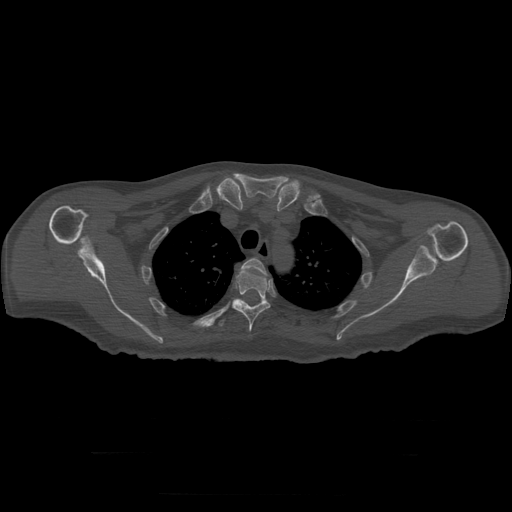
CT including the spine, one axial slice. Position 242 of 397 along the scan axis. Reconstruction kernel STANDARD. Bone window (W 1800 / L 400 HU). 1.25 mm slice thickness. 512 × 512 image matrix, field of view 510 × 510 mm. Patient age 73 years. From the clinical record (not read from this slice): primary cancer: prostate.
Outlined on this slice (semi-automatically segmented with operator editing):
- T3 vertebra: bounding box [x1, y1, x2, y2] px = [242, 258, 267, 276]
- T4 vertebra: [233, 271, 270, 332]
- T5 vertebra: [219, 299, 246, 327]